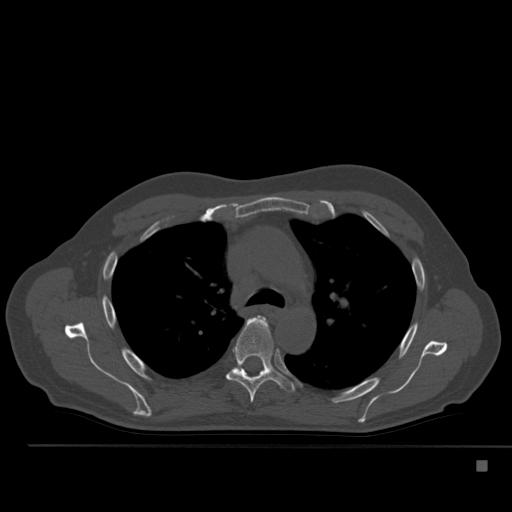
CT including the spine, one axial slice. Bone window (W 1800 / L 400 HU). 1.5 mm slice thickness. 512 × 512 image matrix, field of view 408 × 408 mm. Patient: male, 70 years. From the clinical record (not read from this slice): primary cancer: renal; vertebrae with lytic lesions (as recorded): T4, T6, T10, T12, L3, L4, L5.
Structures marked on this image (semi-automatically segmented with operator editing):
- T5 vertebra: bounding box [x1, y1, x2, y2] px = [226, 318, 294, 403]
- T6 vertebra: [235, 368, 239, 369]